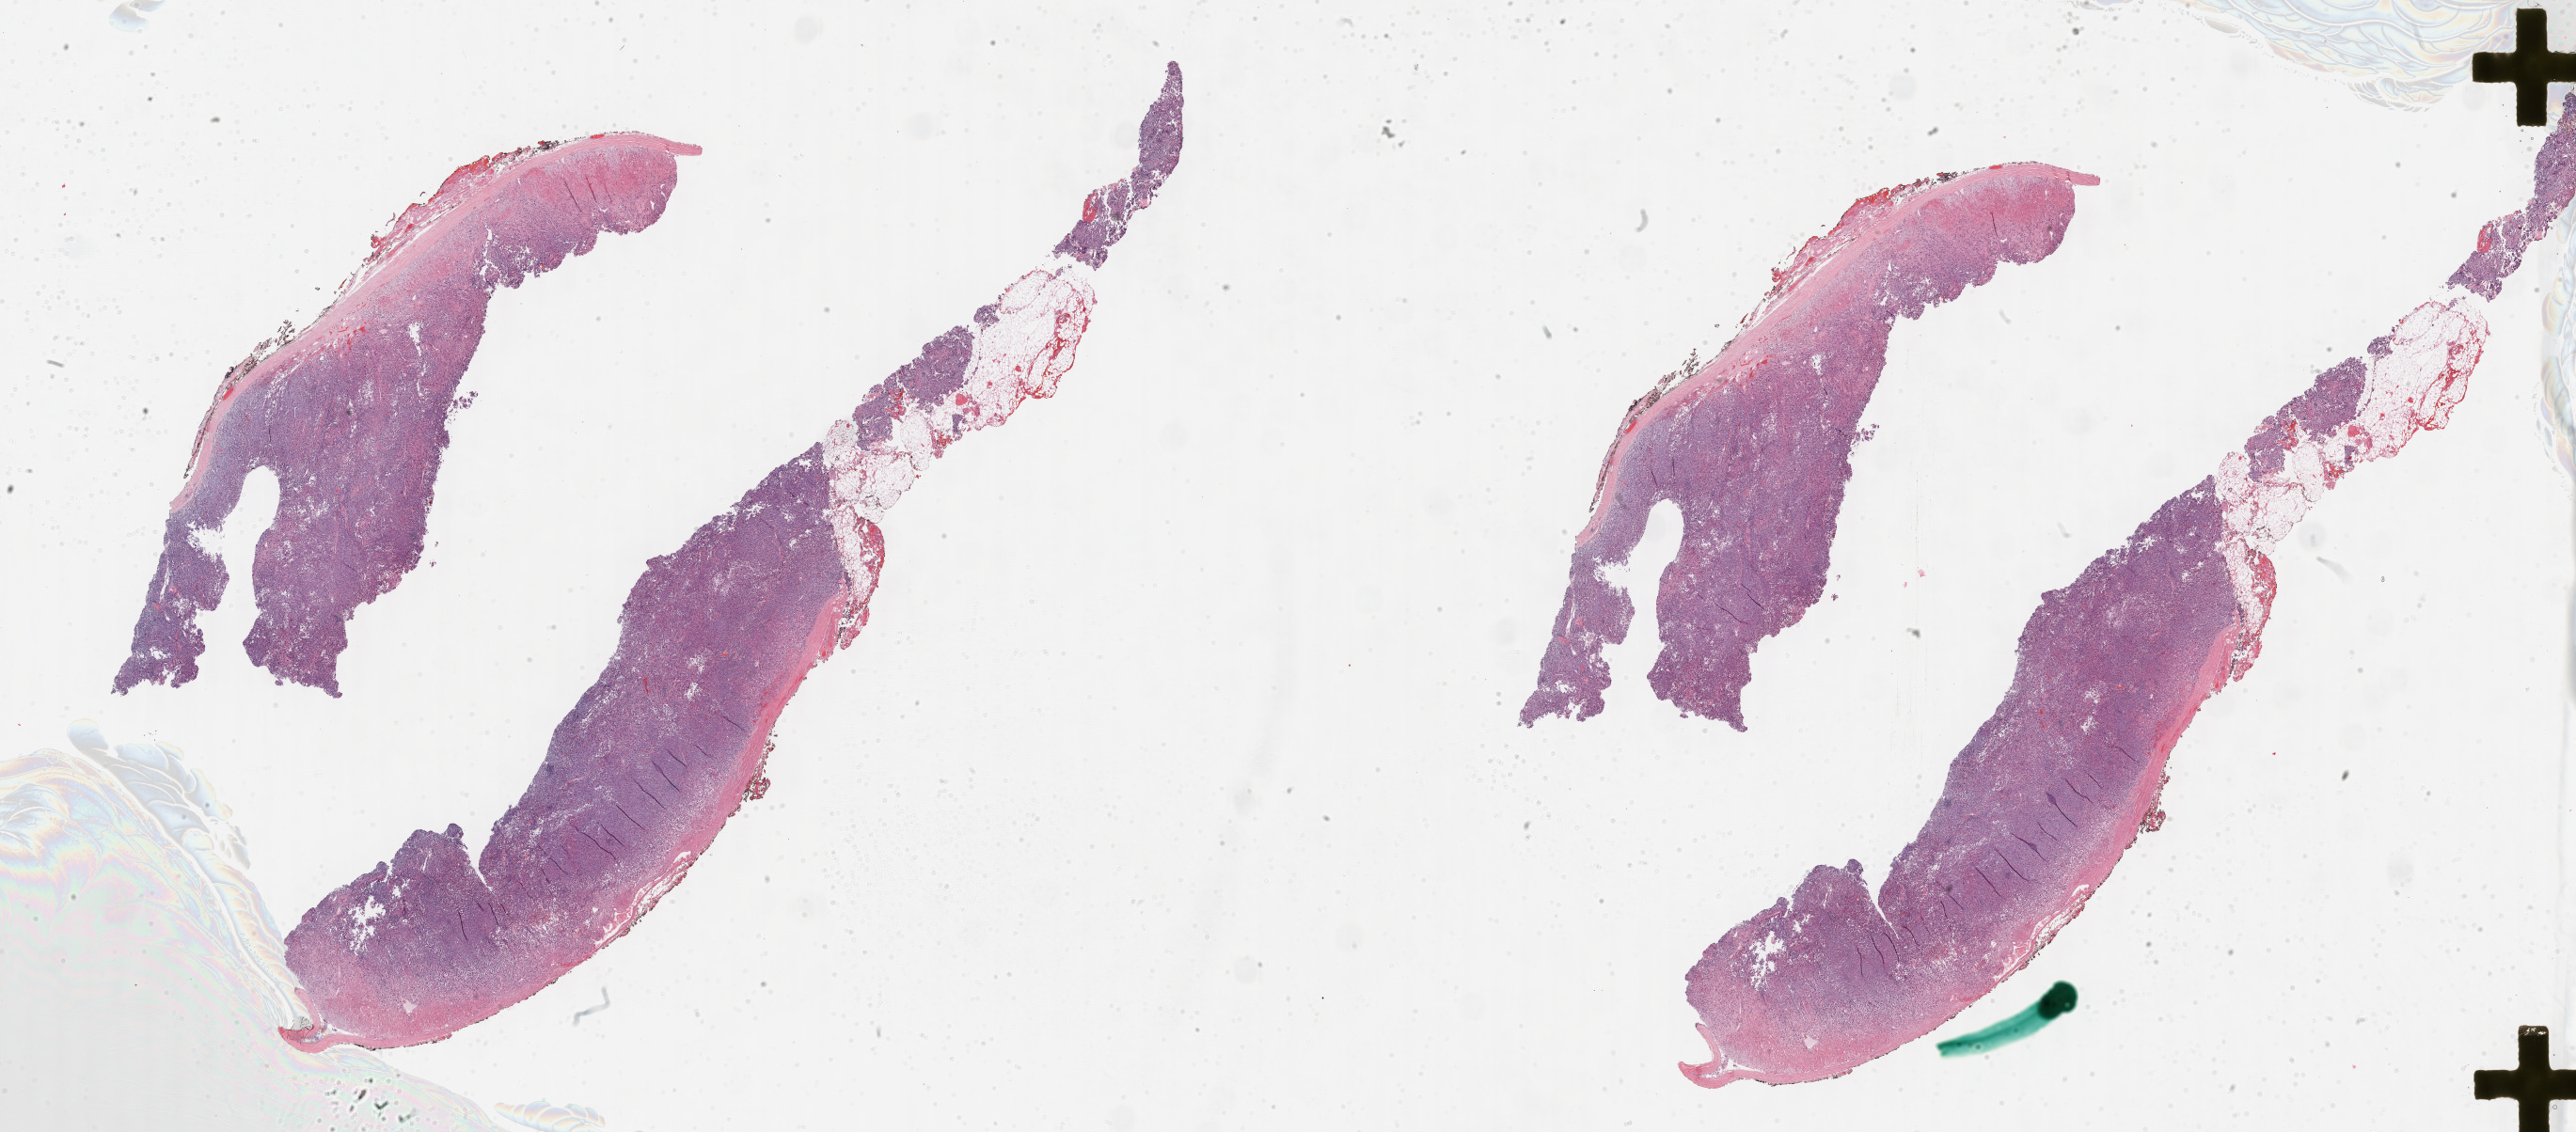
H&E-stained whole-slide image, low-resolution overview of the scanned area, about 44.3 x 19.5 mm (acquisition: 40x scan), FFPE section, sample: primary tumour, adrenal gland. Female, age 49 years at initial diagnosis.
• pathologic diagnosis: Pheochromocytoma, malignant